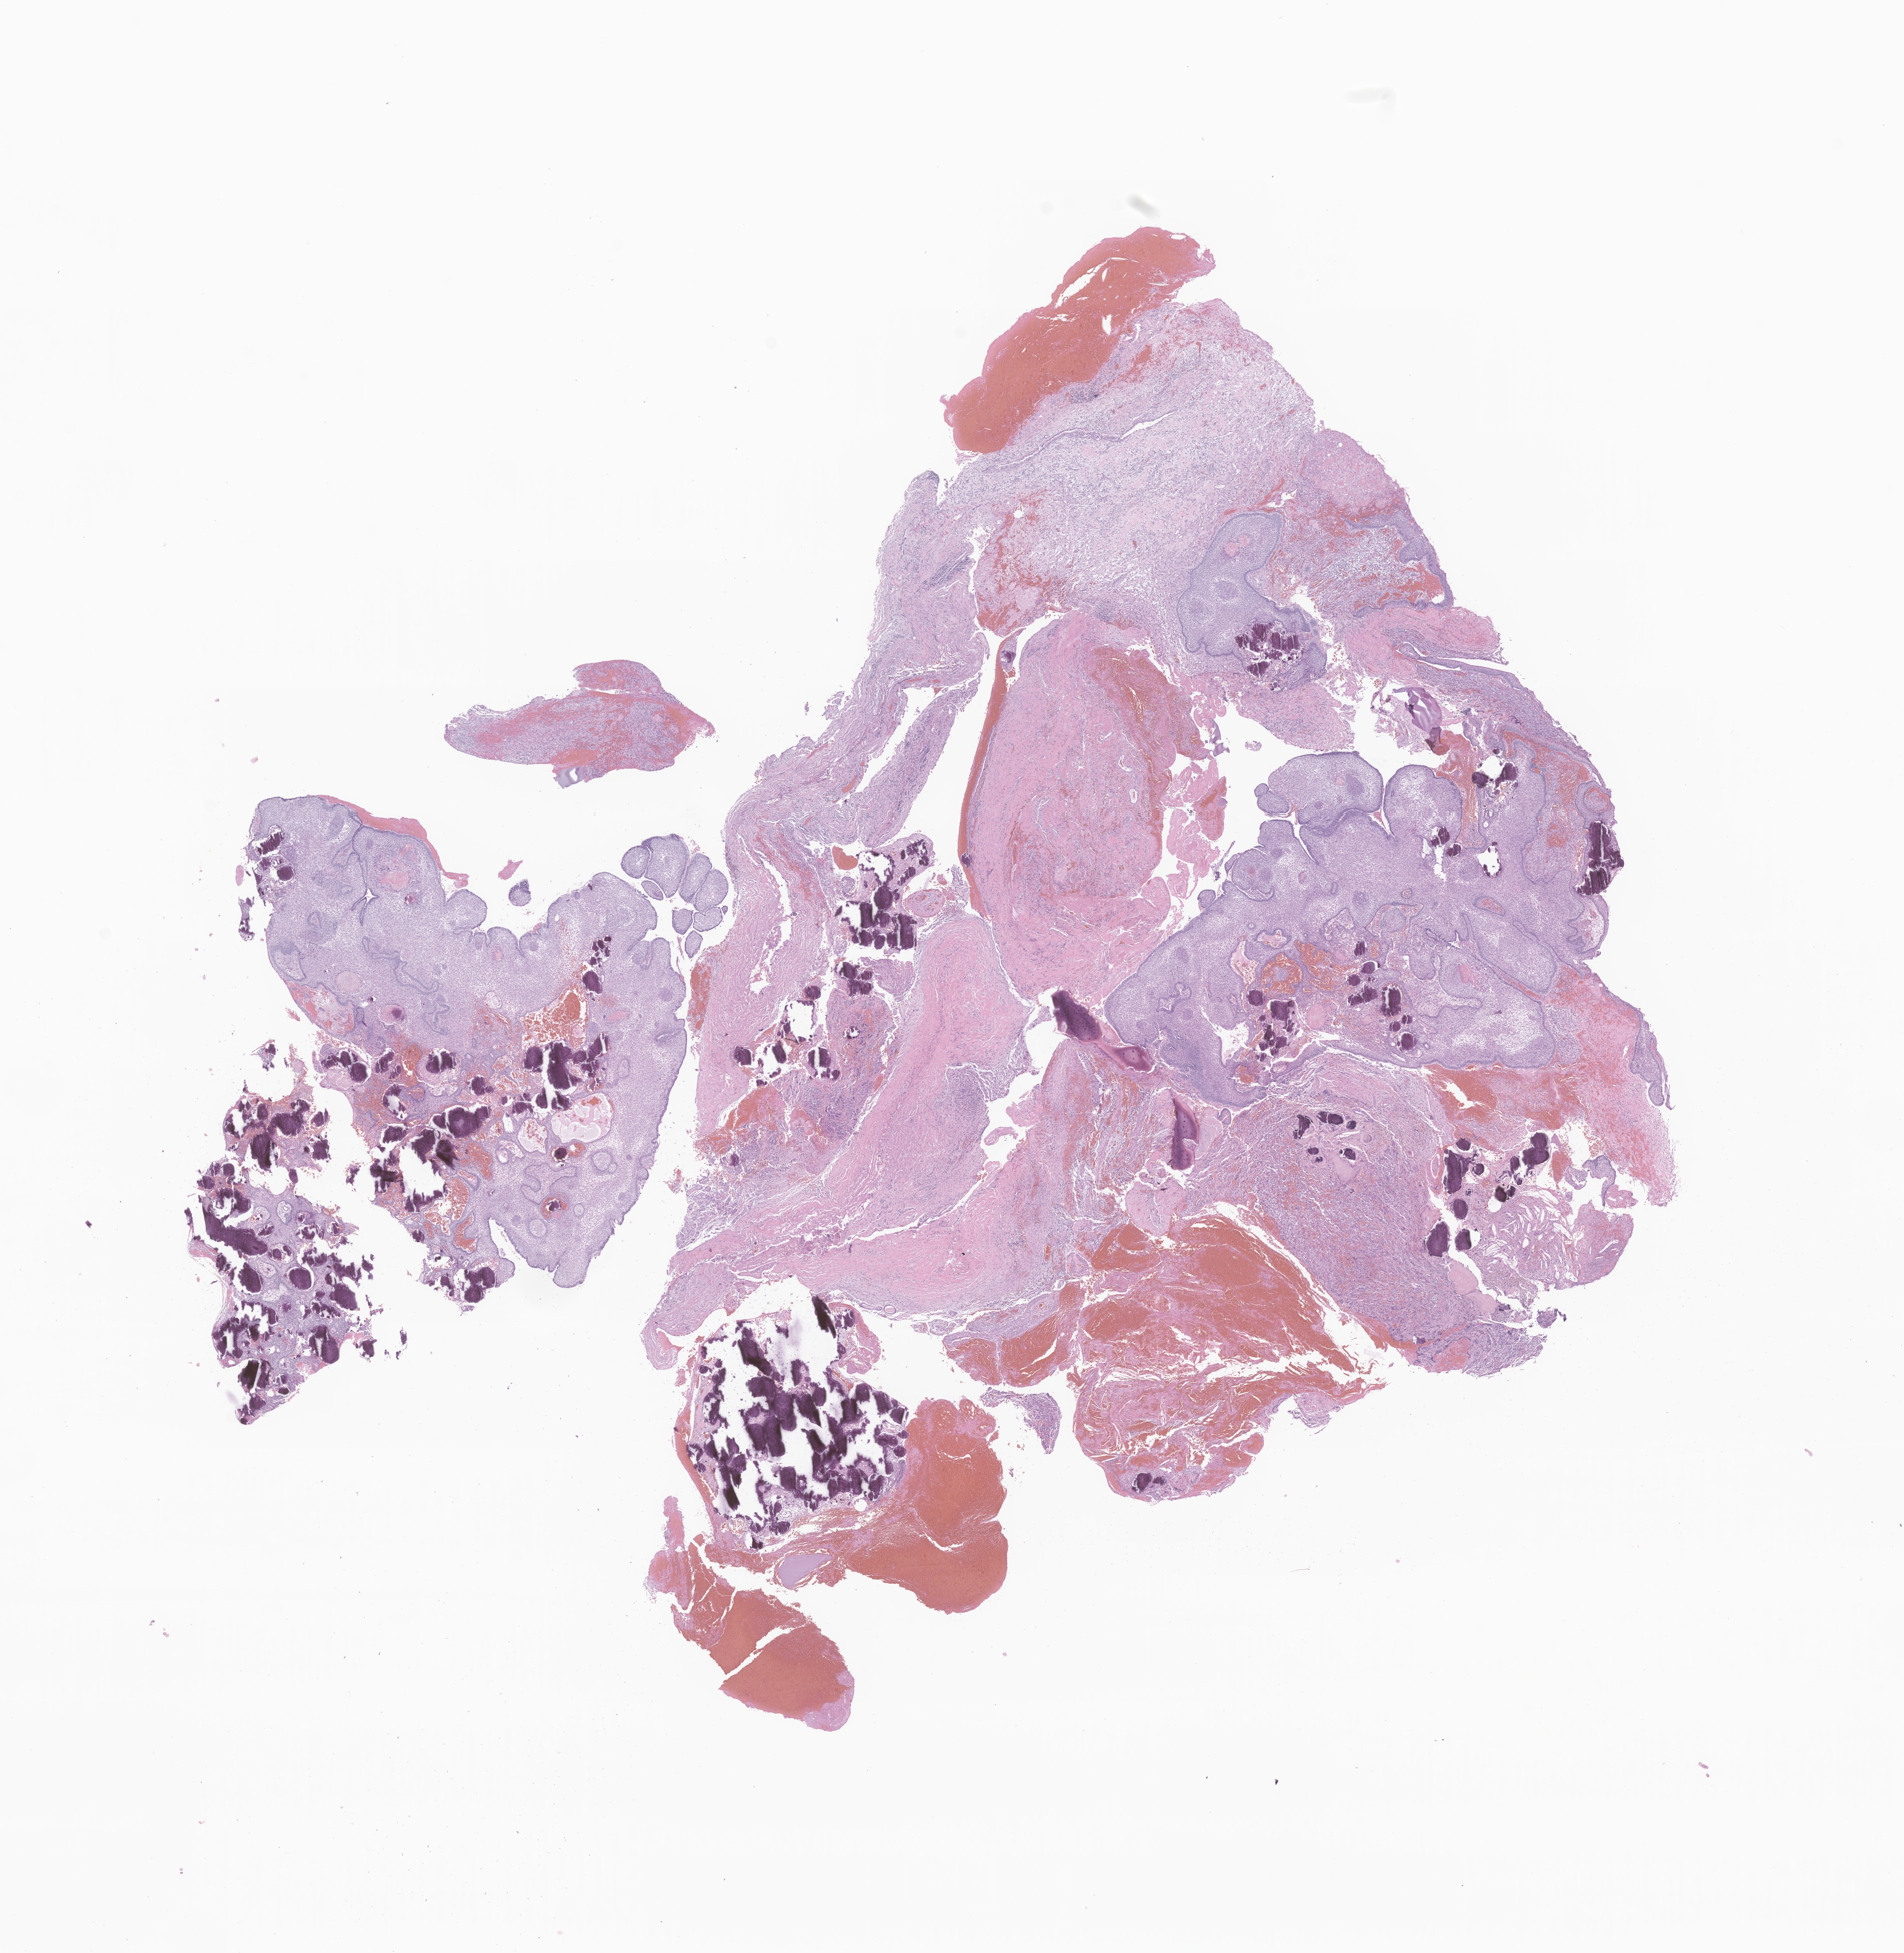
Whole-slide image, H&E stain of tumor tissue from the brain, a low-resolution overview of the entire scanned area, about 16.0 x 16.4 mm. Formalin-fixed paraffin-embedded section. Patient male; age 91 months (7 years 7 months).
* recorded diagnosis: Craniopharyngioma, adamantinomatous